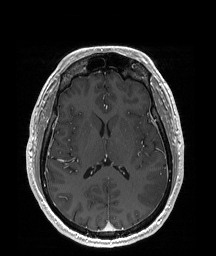
Brain MRI from a brain-tumour surgery series, one axial slice. Position 93 of 192 along the scan axis. T1-weighted post-contrast. 1 mm slice thickness. 216 × 256 image matrix, field of view 219 × 260 mm. From the clinical record (not read from this slice): histopathology: Glioblastoma; WHO grade: 4; IDH mutation: no.
Outlined on this slice (manually delineated by an expert):
- tumour: bounding box [x1, y1, x2, y2] px = [137, 172, 168, 210]